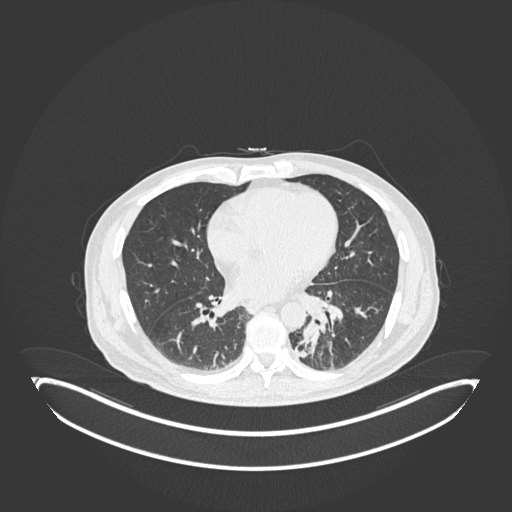
Chest CT, one axial slice; slice 68 of 251 in the series (ordered by position); reconstruction kernel B30f; 120 kVp; lung window (W 1500 / L -600 HU); 1 mm slice thickness; 512 × 512 image matrix. Patient: male, 72 years. Case-level facts recorded for this patient, not image findings: clinical TNM (as recorded): T2b N0 M1.
Outlined on this slice (bounding box drawn by a radiologist):
- lung tumour (recorded histology: adenocarcinoma): box from (x=297, y=319) to (x=320, y=362) px